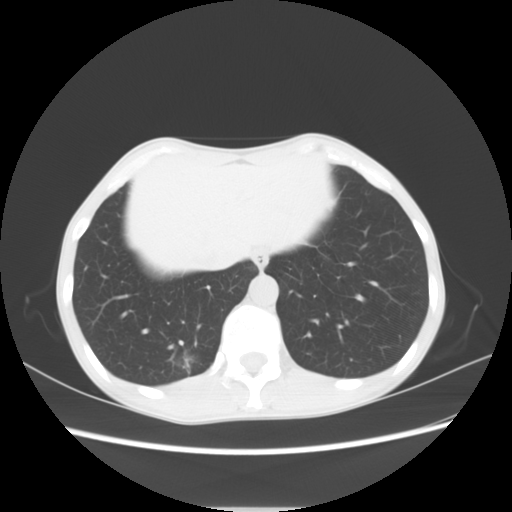
Chest CT, one axial slice; reconstruction kernel STANDARD; 120 kVp; lung window (W 1500 / L -600 HU); 5 mm slice thickness; 512 × 512 image matrix. Female patient, age 51 years. From the clinical record (not read from this slice): clinical TNM (as recorded): T1c N0 M0.
Annotated regions visible in this slice (rectangle marked by the reading radiologist):
- lung tumour (recorded histology: adenocarcinoma): box from (x=169, y=341) to (x=209, y=387) px